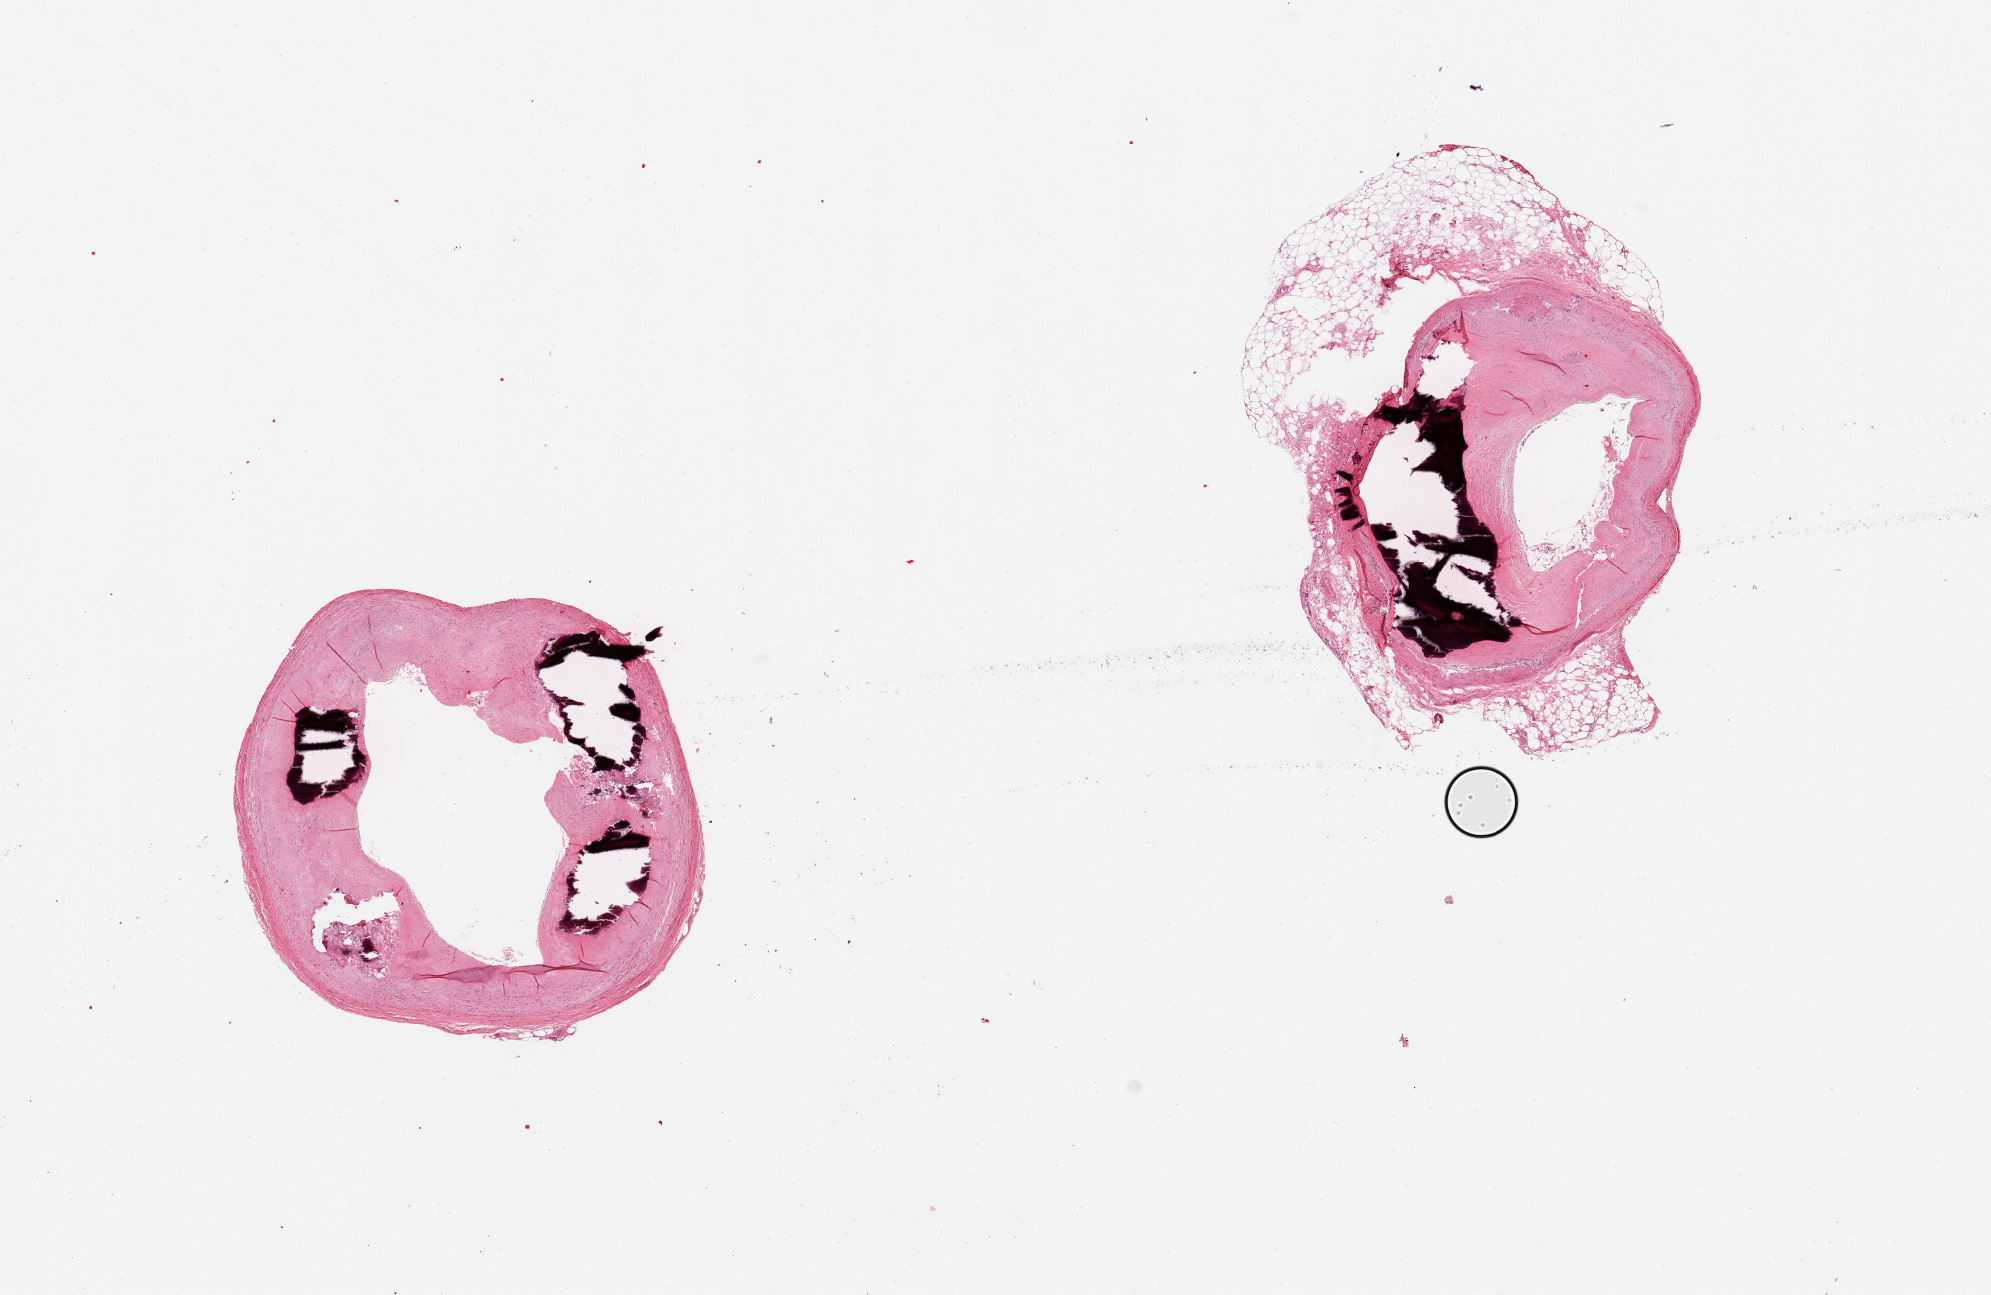
Whole-slide image, H&E stain, low-resolution overview of the scanned area, about 15.8 x 10.2 mm; PAXgene-fixed paraffin-embedded (PFPE) section; target tissue: coronary artery; donor tissue sample.
Review note (as recorded): 2 pieces; severe calcific atherosclerosis with narrowing of the lumen by up to 80%, one piece includes ~50% attached fat.